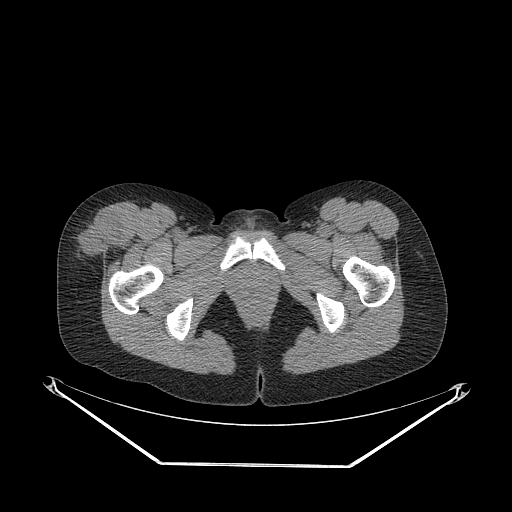
CT of an extremity soft-tissue mass (from a PET/CT study), one axial slice; position 57 of 267 along the scan axis; 140 kVp; soft-tissue window (W 400 / L 40 HU); 3.75 mm slice thickness; 512 × 512 image matrix, field of view 500 × 500 mm. Female patient. Case-level facts recorded for this patient, not image findings: histological type: synovial sarcoma; grade: intermediate; site of the primary tumour: right thigh.
Annotated regions visible in this slice (expert contour drawn on MRI and transferred to this co-registered scan by the dataset authors):
- gross tumour volume including surrounding oedema: bounding box [x1, y1, x2, y2] px = [73, 214, 120, 257]
- gross tumour volume (mass): [73, 214, 120, 257]